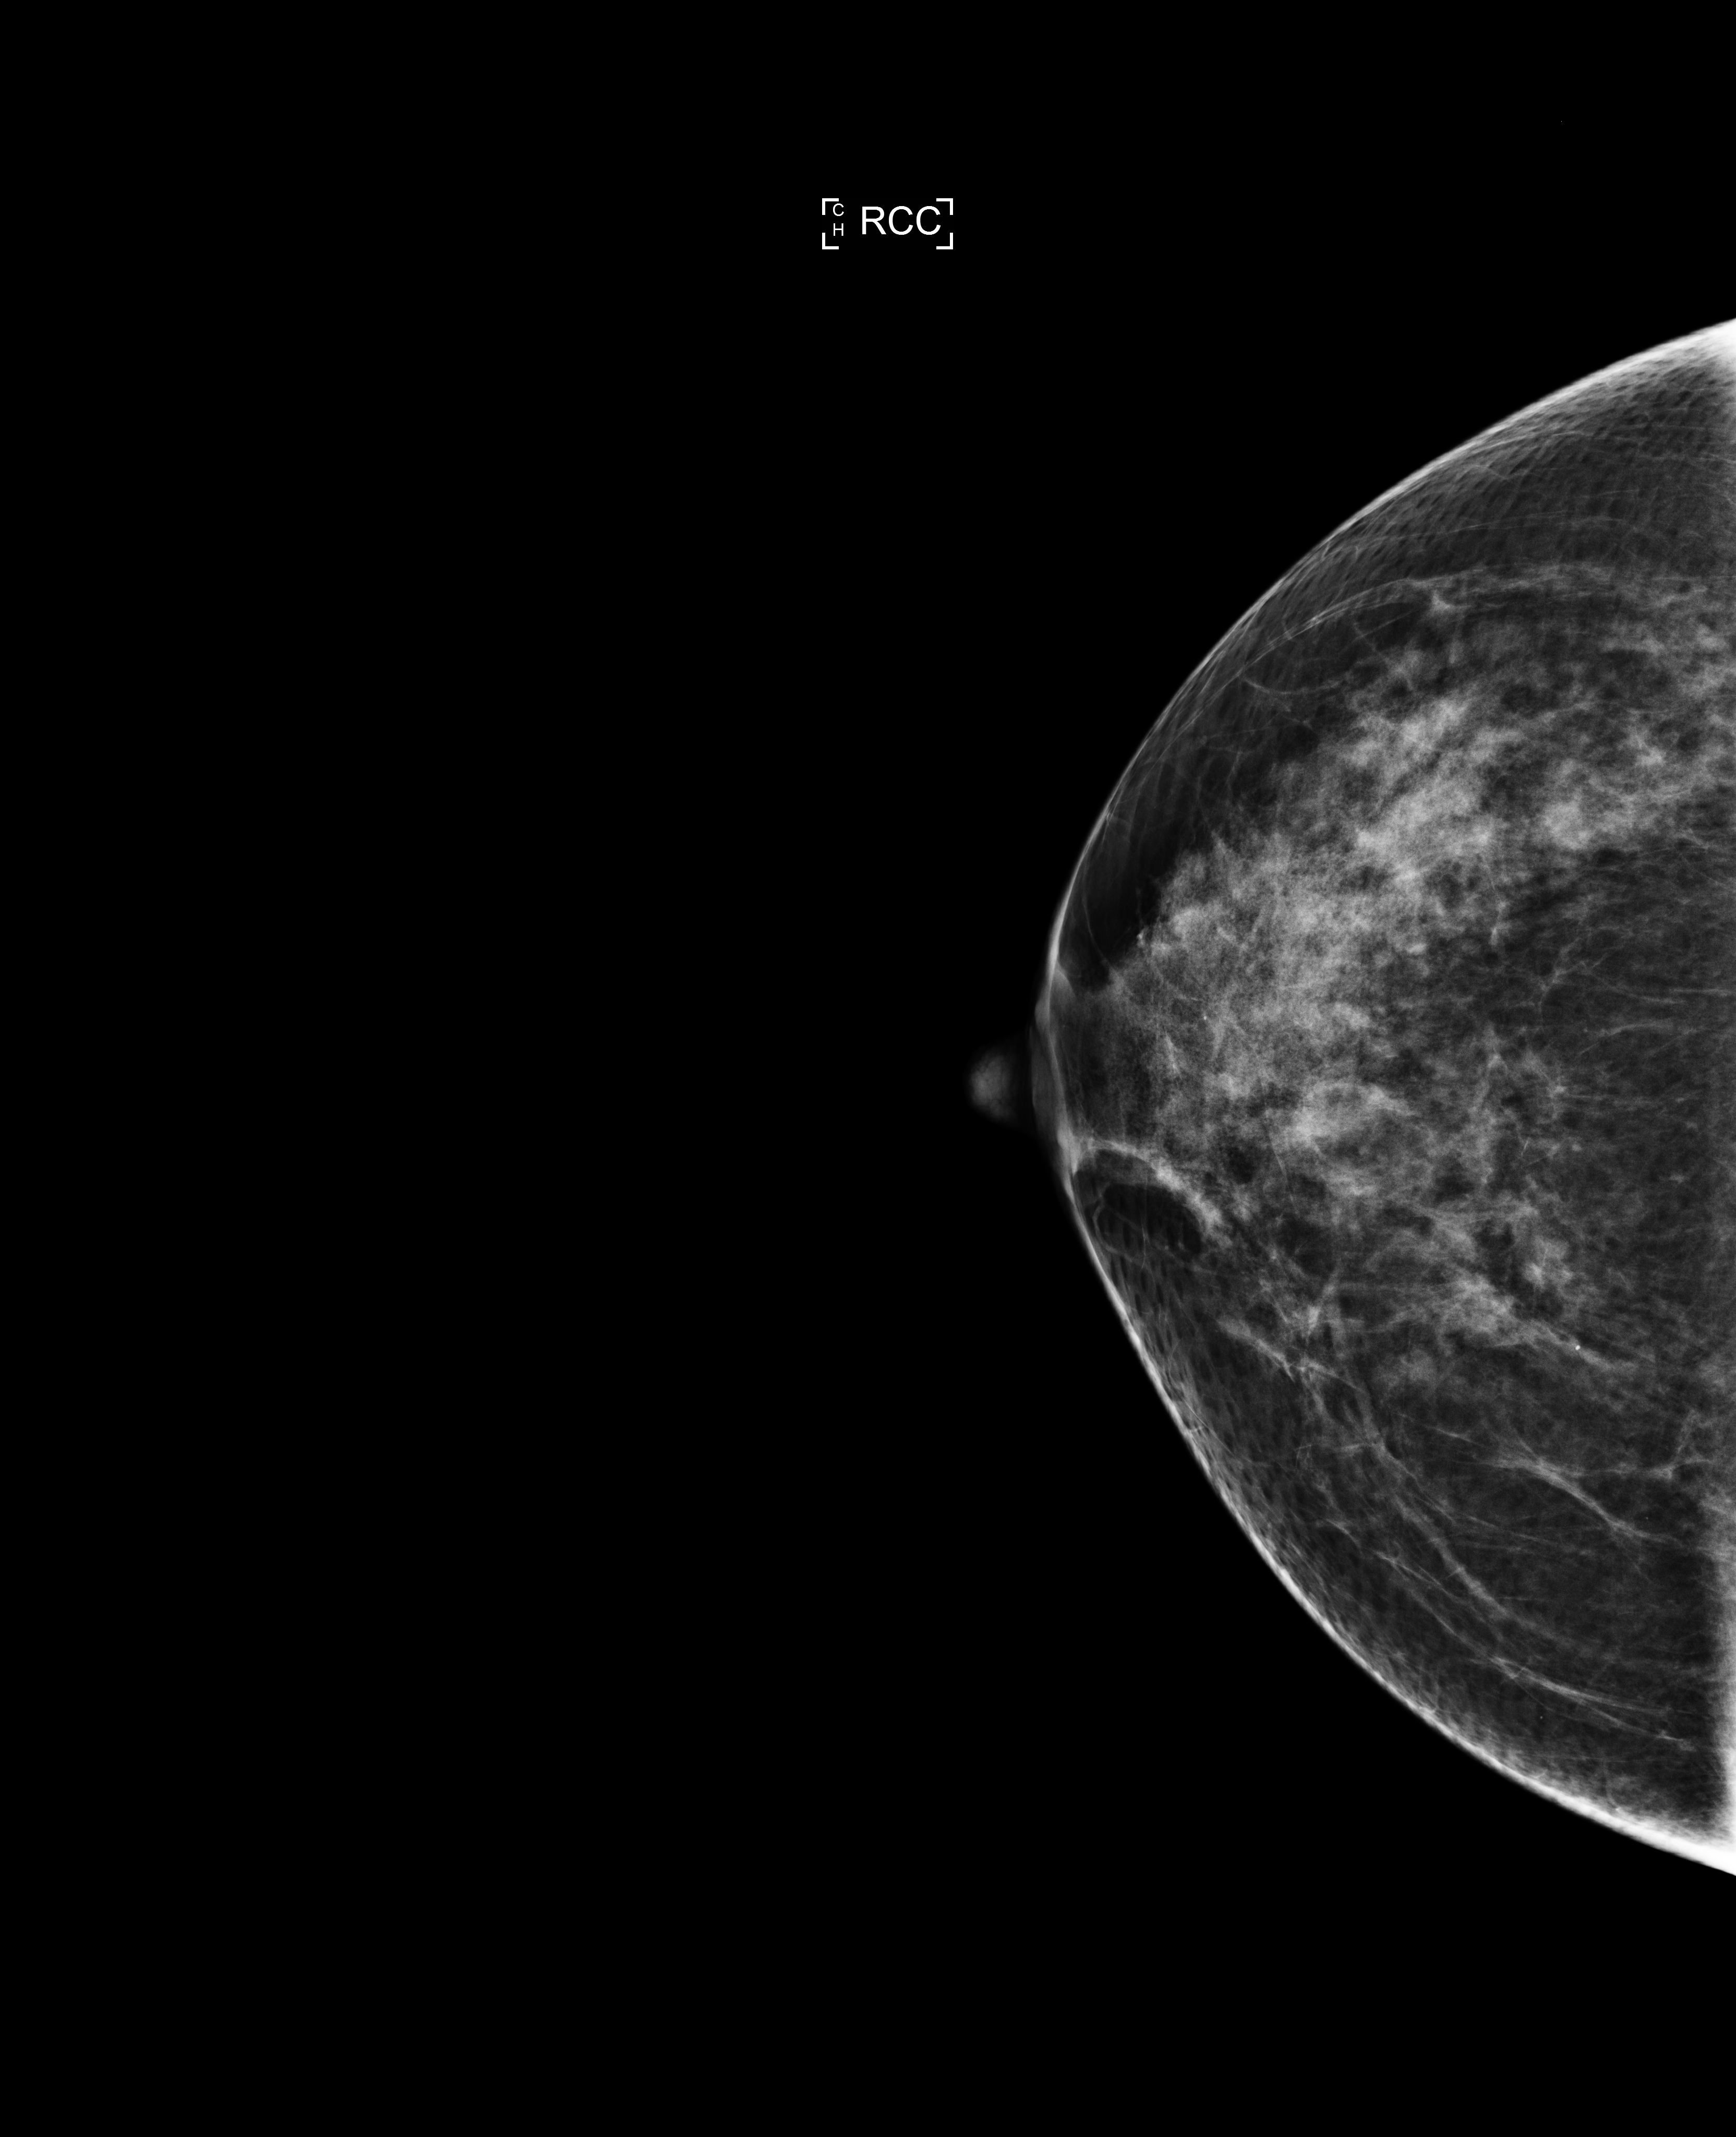
Digital mammogram (FFDM), right breast, cranio-caudal projection, annual screening mammography examination, compressed breast thickness 78 mm, system: Selenia Dimensions. Female patient, age 49 years.
- breast density at the screening exam (both breasts): heterogeneously dense (BI-RADS density category c)
- final BI-RADS assessment for this screening round (tomosynthesis exam, both breasts): category 1
- recall: no recall after this screen